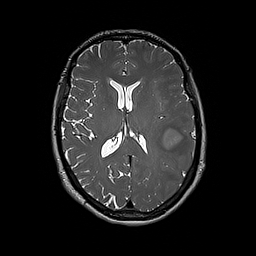
Brain MRI from a brain-tumour surgery series, one axial slice. Slice 93 of 192 in the series (ordered by position). 256 × 256 image matrix. Case-level facts recorded for this patient, not image findings: histopathology: Glioblastoma; WHO grade: 4; IDH mutation: no; tumour location: Left Frontal.
Annotated regions visible in this slice (outlined manually by an expert reader):
- tumour: box from (x=164, y=121) to (x=195, y=170) px